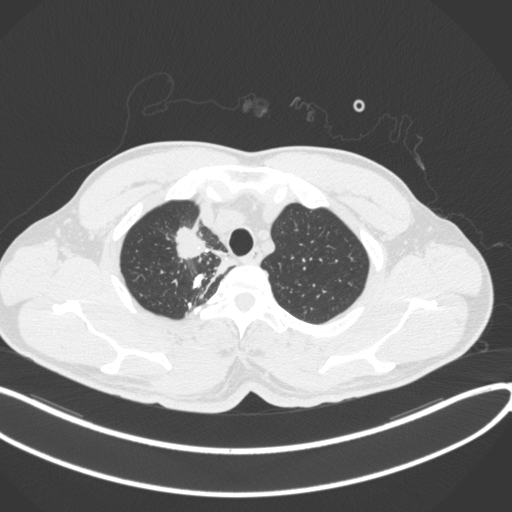
Chest CT, one axial slice. Slice 323 of 391 in the series (ordered by position). Reconstruction kernel B31f. 120 kVp. Lung window (W 1500 / L -600 HU). 1 mm slice thickness. 512 × 512 image matrix, field of view 400 × 400 mm. Patient: male, 48 years. Case-level facts recorded for this patient, not image findings: clinical TNM (as recorded): T1c N1 M1.
Annotated regions visible in this slice (rectangle marked by the reading radiologist):
- lung tumour (recorded histology: adenocarcinoma): bounding box [x1, y1, x2, y2] px = [170, 221, 215, 261]